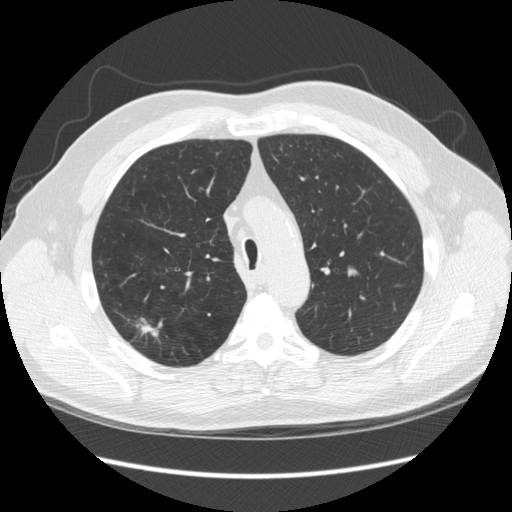
Chest CT (low-dose screening protocol), one axial image; third screening round (two years after baseline); lung window (W 1500 / L -600 HU); slice 66 of 248 in the series. Male, age 64 years at enrolment. Former smoker at enrolment.
Lesion marked by an expert reader, bounding box <117,314,170,357> (left, top, right, bottom; pixels). The screening reader recorded 4 non-calcified nodules or masses ≥4 mm on this exam (right upper lobe, right upper lobe, right upper lobe, right upper lobe); which of them this box marks is not recorded. Later outcome: lung cancer diagnosed 15 days after this screen — adenocarcinoma, NOS, right upper lobe, moderately differentiated (G2), stage IA (AJCC 6th edition), 14 mm at pathology.